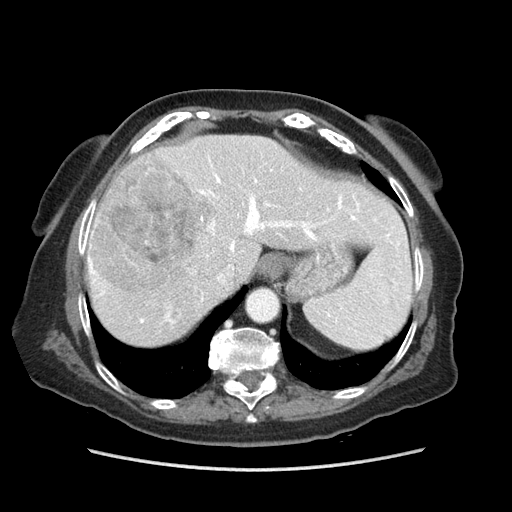
Contrast-enhanced abdominal CT (liver protocol), one axial slice; slice 64 of 89 in the series (ordered by position); soft-tissue window (W 400 / L 40 HU); 2.5 mm slice thickness; 512 × 512 image matrix, field of view 360 × 360 mm. From the clinical record (not read from this slice): diagnosis: hepatocellular carcinoma (patient treated with transarterial chemoembolisation; whether this scan precedes or follows treatment is not stated here); TNM stage (as recorded): Stage-IIIA; Child-Pugh class: A; tumour nodularity: multinodular.
Outlined on this slice (semi-automatic segmentation, software-assisted and operator-edited):
- abdominal aorta: box from (x=247, y=290) to (x=277, y=320) px
- liver parenchyma outside the tumour (the mass and vessels are separate outlines, so this box may not span the whole liver): (x=82, y=134)–(x=406, y=346)
- mass: (x=91, y=155)–(x=215, y=292)
- liver vessels: (x=83, y=157)–(x=394, y=324)